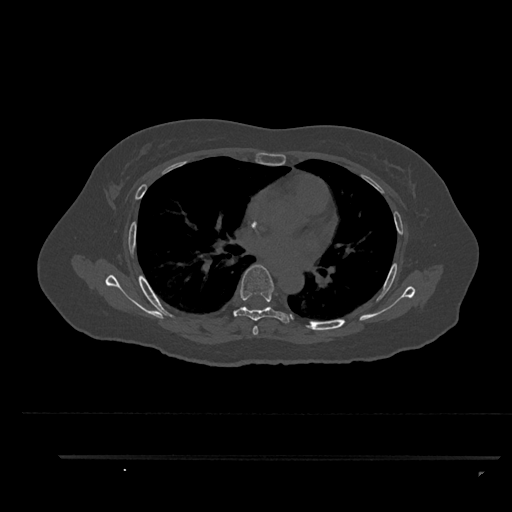
CT including the spine, one axial slice; slice 560 of 797 in the series (ordered by position); 120 kVp; bone window (W 1800 / L 400 HU); 0.5 mm slice thickness; 512 × 512 image matrix, field of view 408 × 408 mm. Patient: female, 44 years. Case-level facts recorded for this patient, not image findings: primary cancer: renal.
Annotated regions visible in this slice (semi-automatically segmented with operator editing):
- T5 vertebra: bounding box <253,326,258,335> (left, top, right, bottom; pixels)
- T6 vertebra: <223,264,292,335>